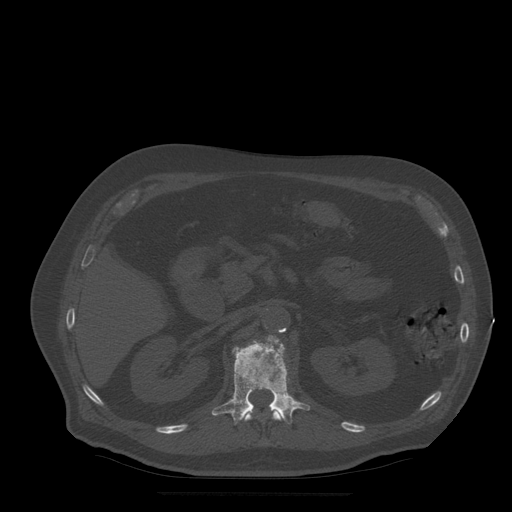
CT including the spine, one axial slice. Position 200 of 522 along the scan axis. Bone window (W 1800 / L 400 HU). 1.25 mm slice thickness. 512 × 512 image matrix. Patient age 72 years. Case-level facts recorded for this patient, not image findings: primary cancer: prostate.
Outlined on this slice (semi-automatically segmented with operator editing):
- L1 vertebra: bounding box [x1, y1, x2, y2] px = [212, 336, 310, 425]
- T12 vertebra: [244, 409, 282, 422]